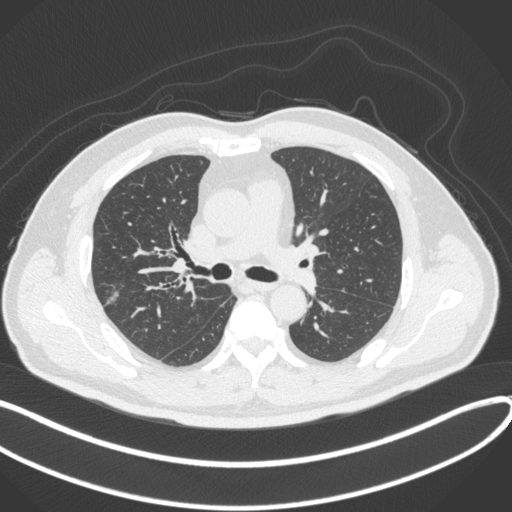
Chest CT, one axial slice; position 209 of 373 along the scan axis; reconstruction kernel B31f; 120 kVp; lung window (W 1500 / L -600 HU); 1 mm slice thickness; 512 × 512 image matrix, field of view 400 × 400 mm. Patient: male, 60 years. From the clinical record (not read from this slice): clinical TNM (as recorded): T1c N0 M0.
Outlined on this slice (bounding box drawn by a radiologist):
- lung tumour (recorded histology: adenocarcinoma): bounding box (x1, y1, x2, y2) in pixels: (103, 282, 134, 309)